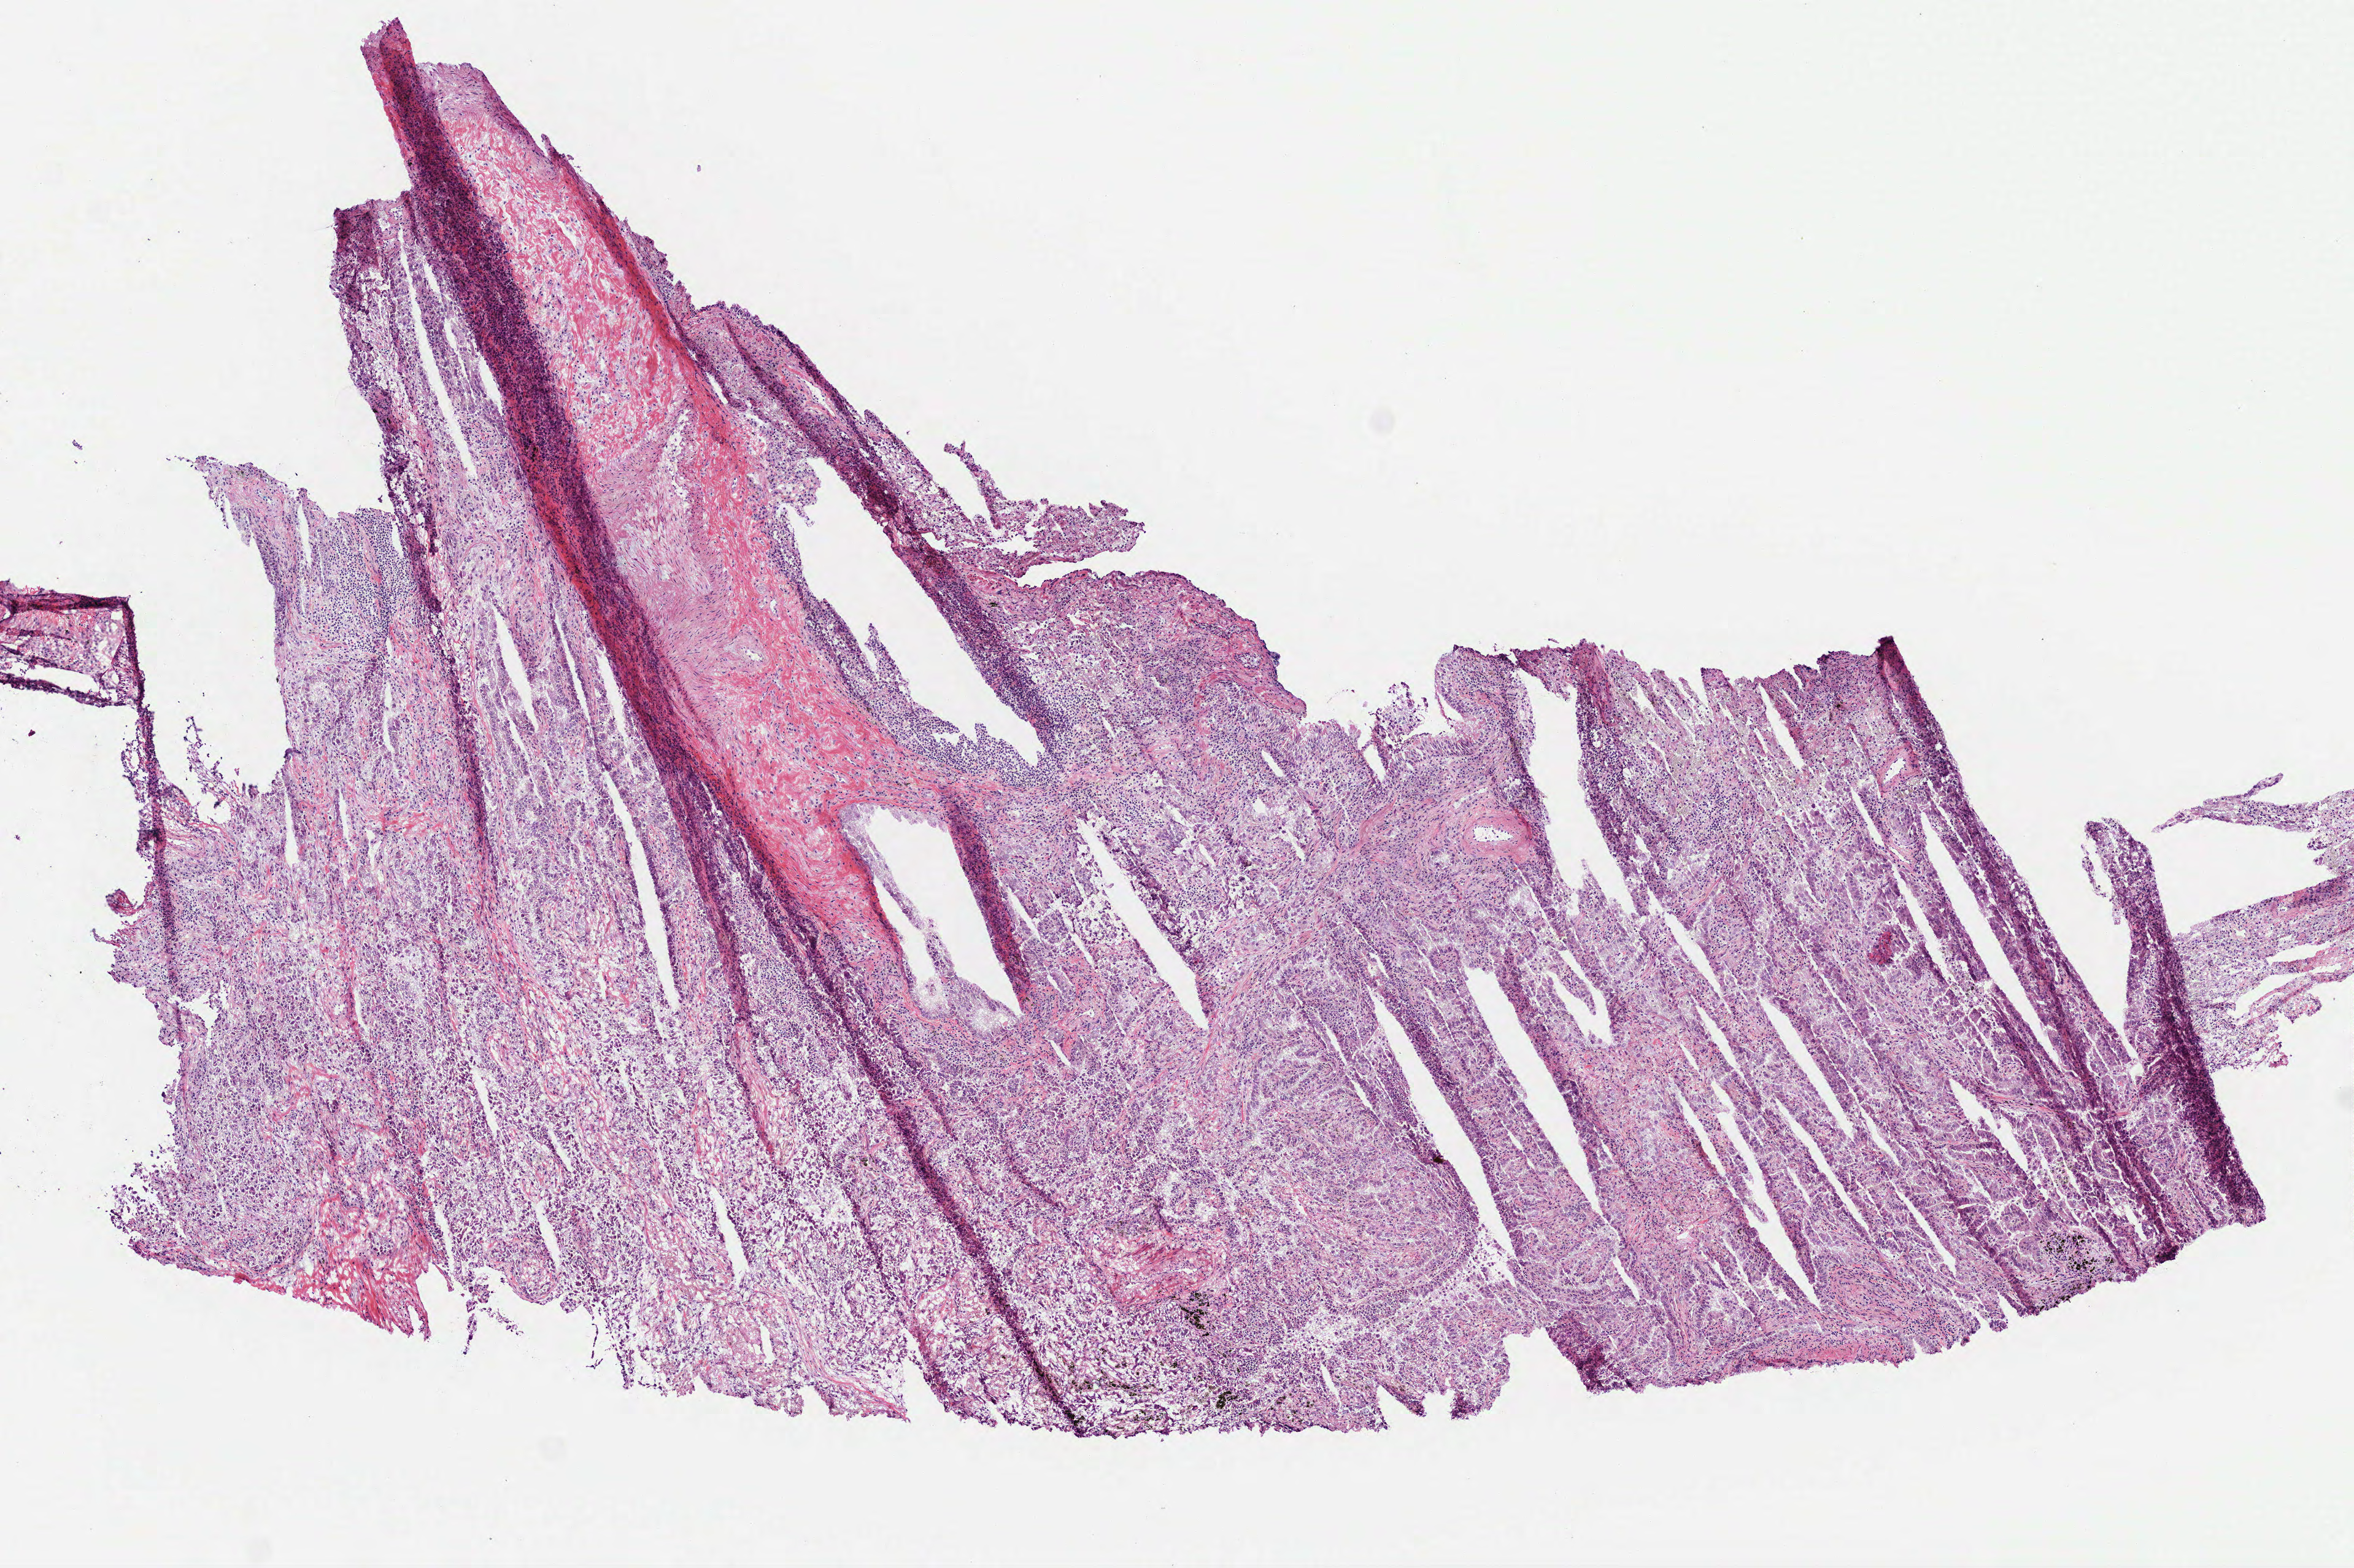
Digitized H&E-stained tissue section (whole slide), a low-resolution overview of the entire scanned area, about 7.7 x 5.2 mm; frozen section from the bottom of the tissue portion; primary tumour sample from the lung. Male, age 56 years at initial diagnosis. Pathologist review of this section (percent, as recorded): tumour cells 85%, tumour nuclei 75%, normal cells 0%, stromal cells 15%, necrosis 0%. Inflammatory infiltration, as recorded: lymphocyte infiltration 20%.
* diagnosis: Adenocarcinoma with mixed subtypes (upper lobe, lung)